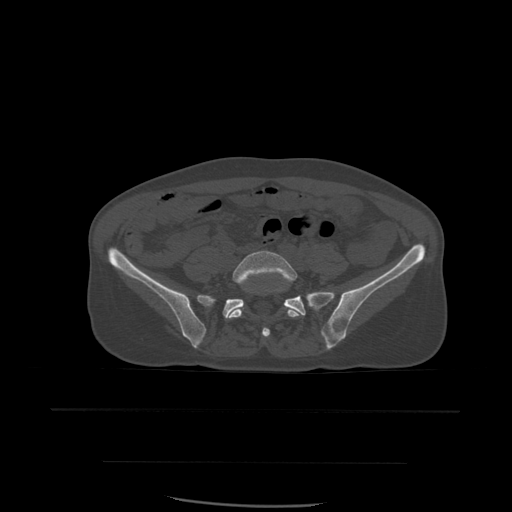
CT including the spine, one axial slice. Position 138 of 574 along the scan axis. Bone window (W 1800 / L 400 HU). 1.25 mm slice thickness. 512 × 512 image matrix, field of view 392 × 392 mm. Patient age 48 years. From the clinical record (not read from this slice): primary cancer: lung; vertebrae with lytic lesions (as recorded): T11.
Annotated regions visible in this slice (semi-automatically segmented with operator editing):
- L5 vertebra: bounding box (x1, y1, x2, y2) in pixels: (227, 250, 304, 337)